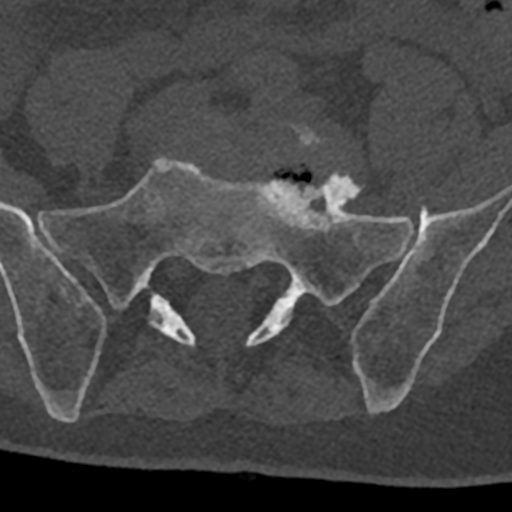
CT including the spine, one axial slice. Slice 150 of 797 in the series (ordered by position). 120 kVp. Bone window (W 1800 / L 400 HU). 0.5 mm slice thickness. 512 × 512 image matrix, field of view 160 × 160 mm. Patient: male, 74 years. Case-level facts recorded for this patient, not image findings: primary cancer: renal; vertebrae with lytic lesions (as recorded): T10, L1, L2, L3, L4, L5.
Structures marked on this image (semi-automatic segmentation, software-assisted and operator-edited):
- L5 vertebra: box from (x=289, y=124) to (x=324, y=148) px